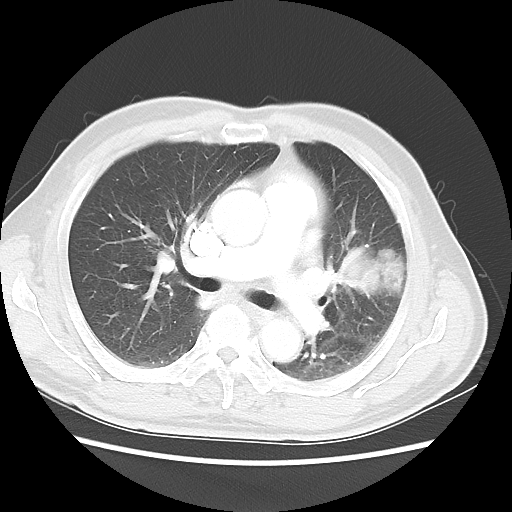
Chest CT, one axial slice. Position 30 of 50 along the scan axis. Reconstruction kernel LUNG. 120 kVp. Lung window (W 1500 / L -600 HU). 5 mm slice thickness. 512 × 512 image matrix, field of view 360 × 360 mm. Male patient, age 69 years. From the clinical record (not read from this slice): clinical TNM (as recorded): T3 N1 M1a.
Outlined on this slice (bounding box drawn by a radiologist):
- lung tumour (recorded histology: squamous cell carcinoma): bounding box [x1, y1, x2, y2] px = [334, 239, 418, 298]